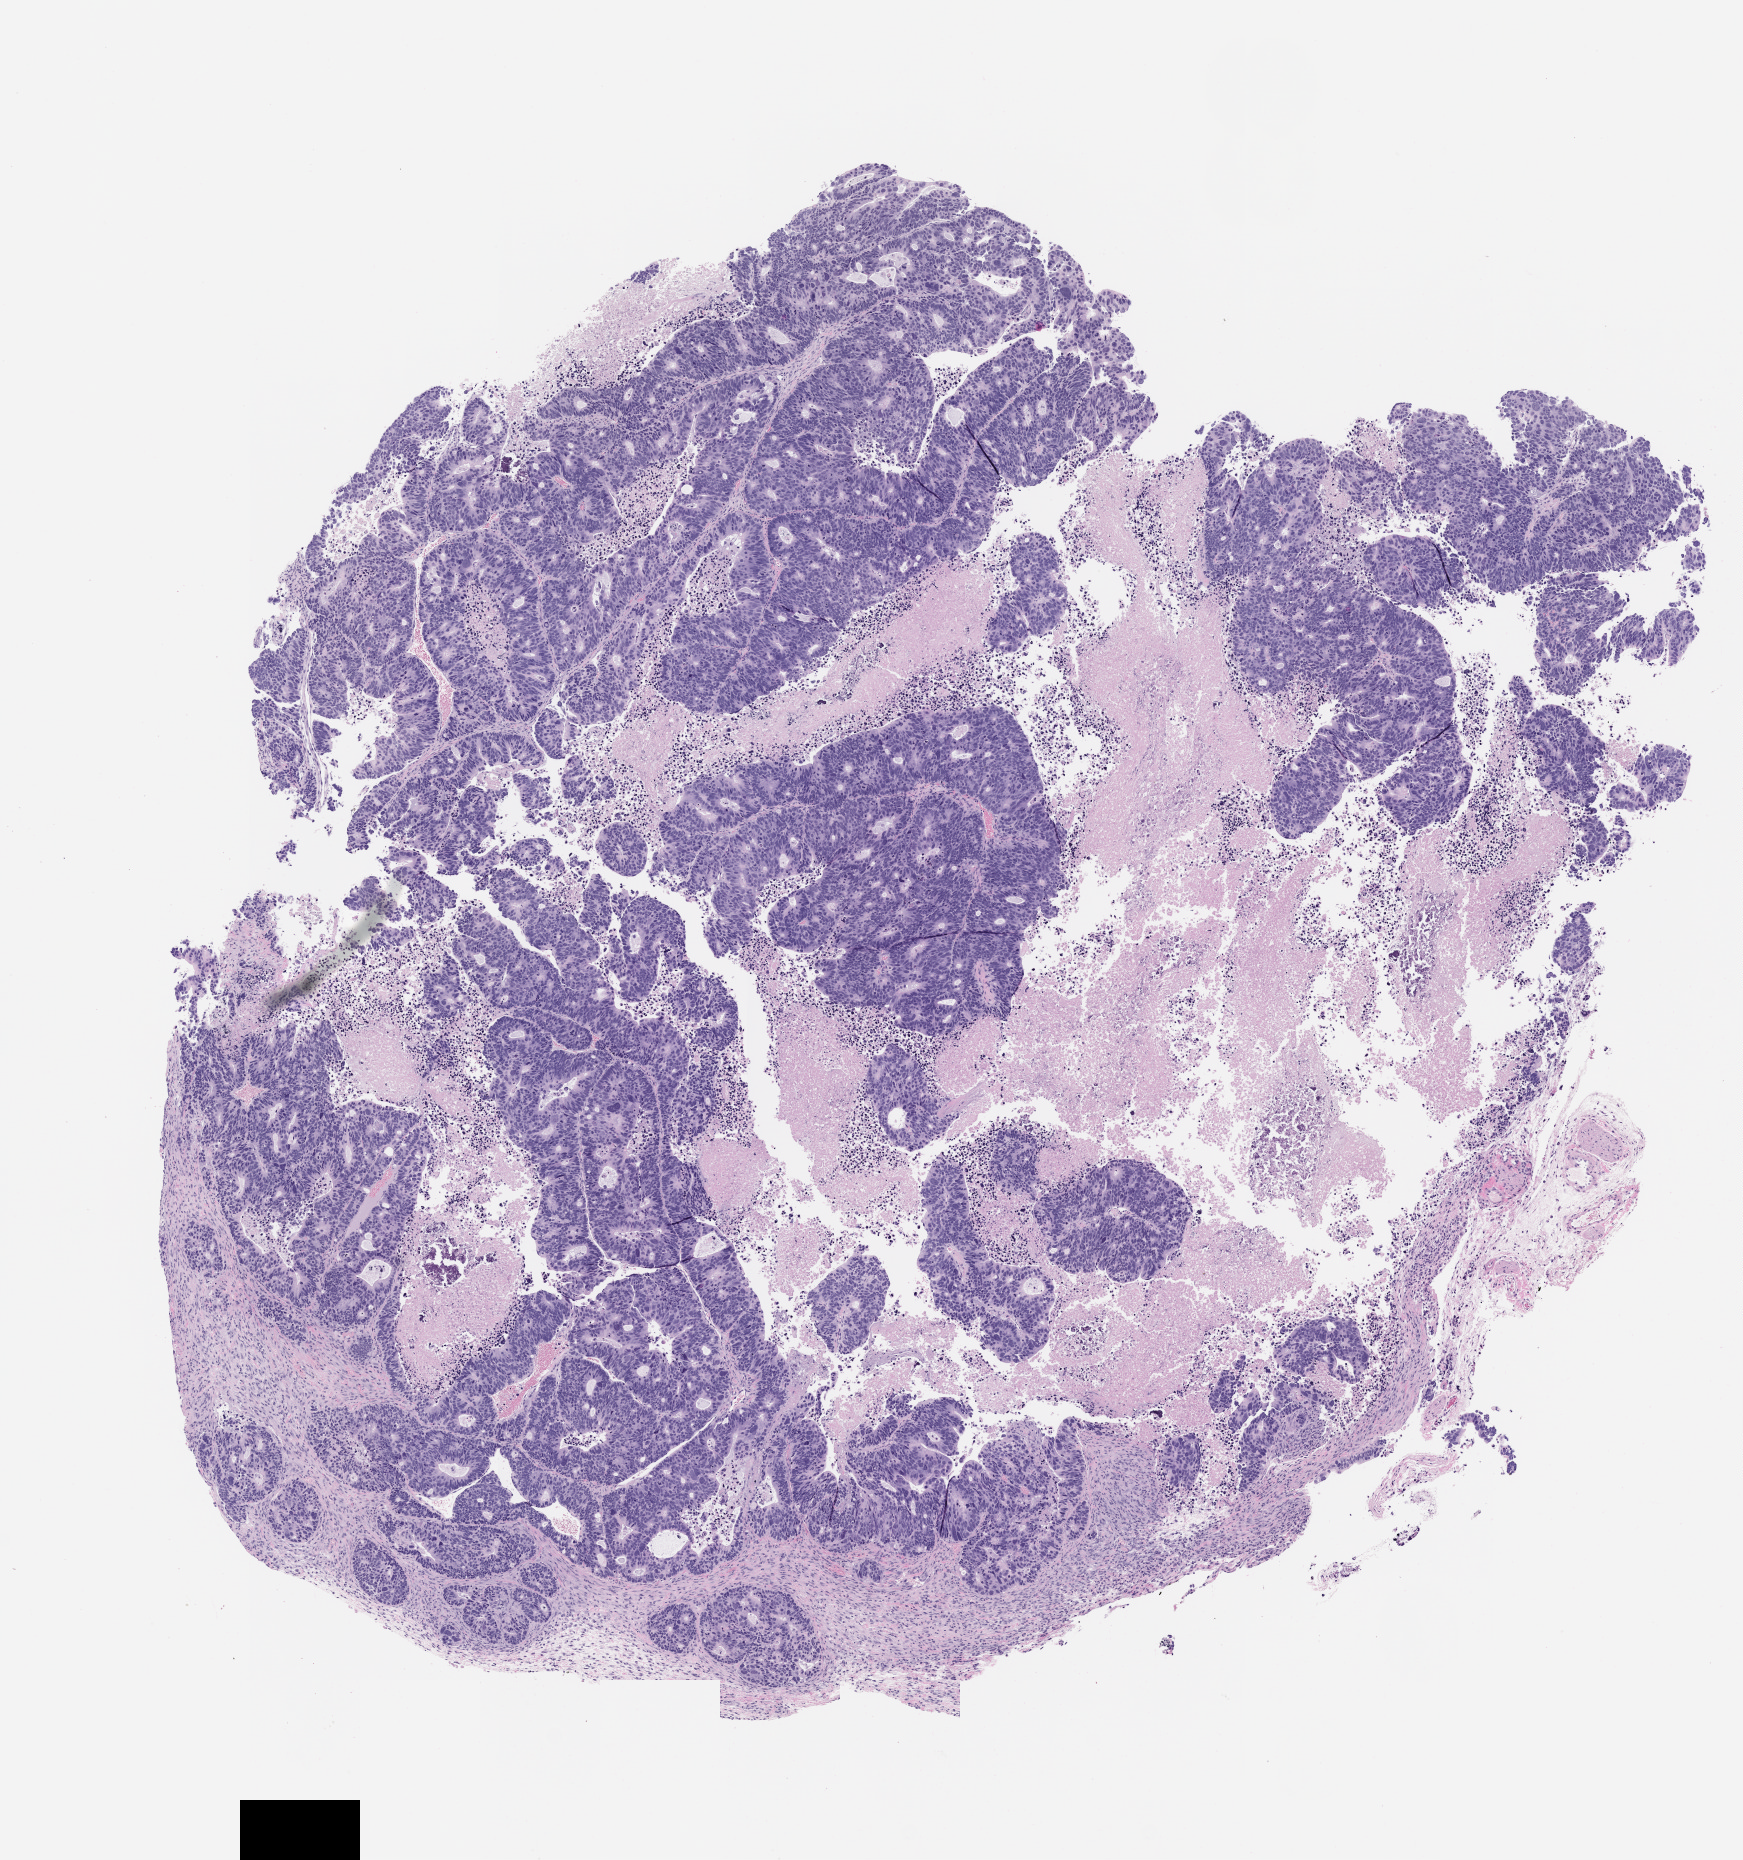
Haematoxylin and eosin whole-slide image of a patient-derived xenograft (PDX) tumor grown in a mouse, passage 1, a low-resolution overview of the entire scanned area, about 7.0 x 7.5 mm; formalin-fixed paraffin-embedded section; tumor site category: colon.
Originating patient diagnosis: Colon Adenocarcinoma.